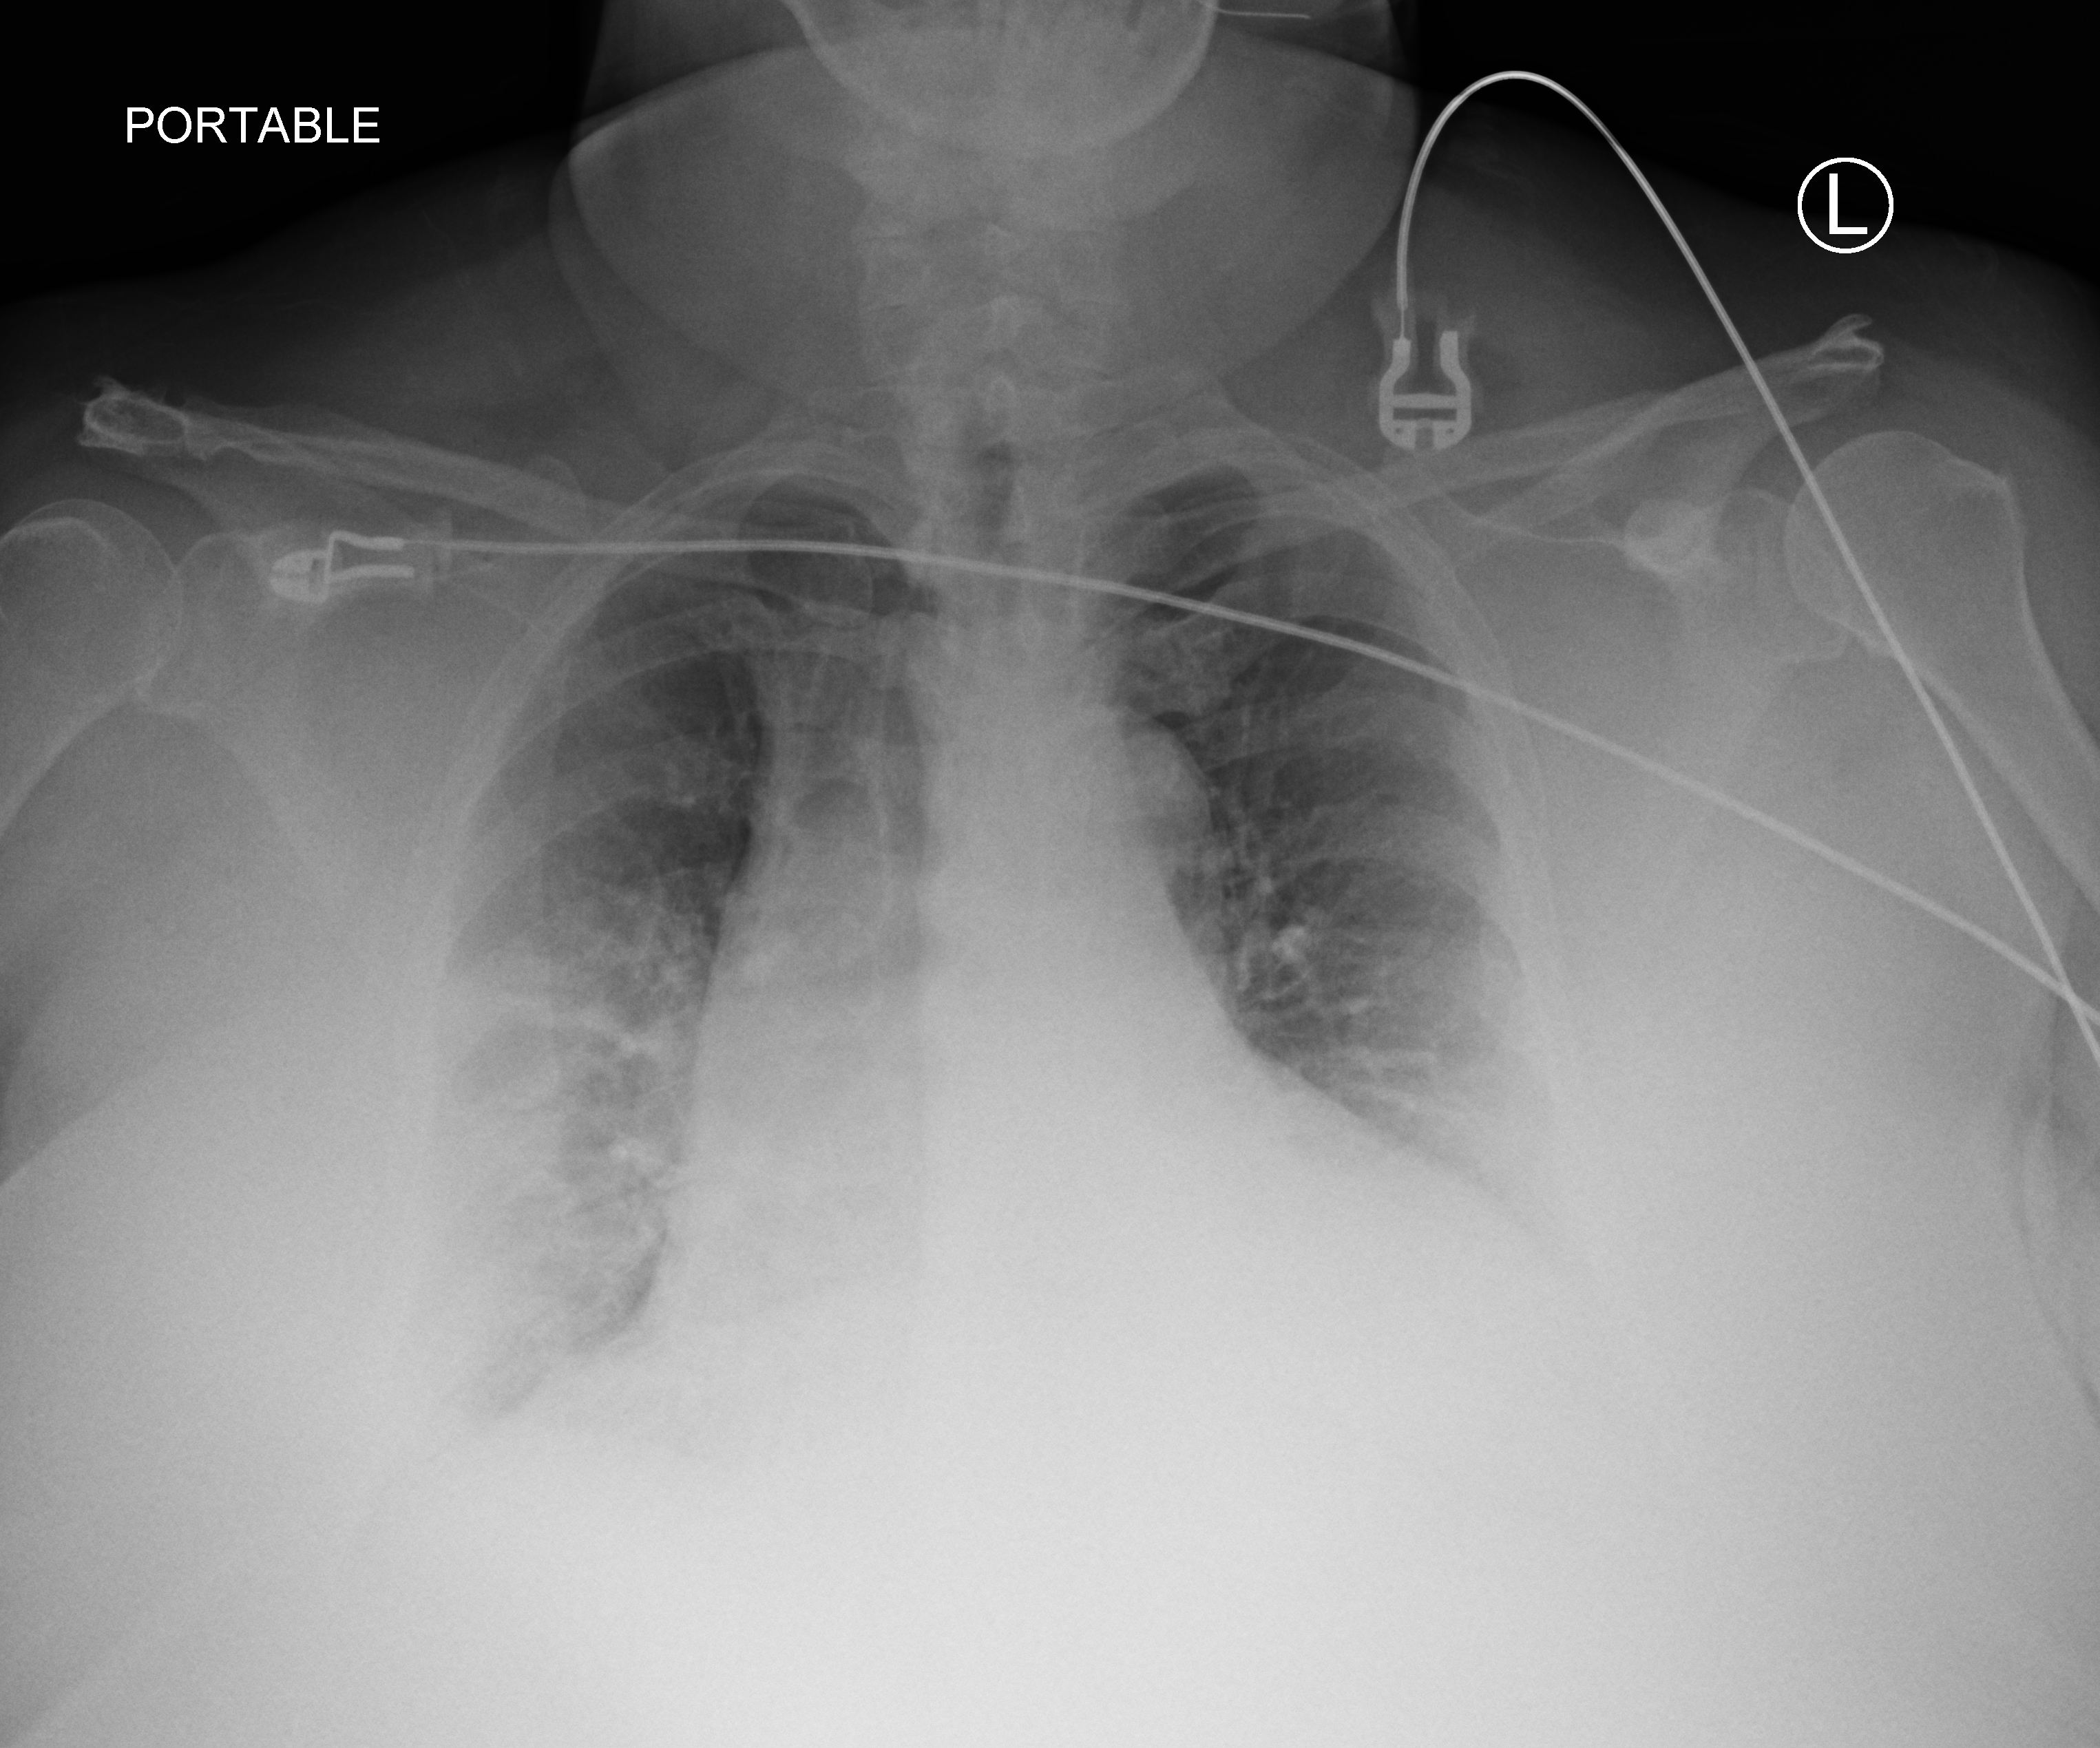
Bedside chest radiograph (computed radiography); anteroposterior (AP) projection. Female patient hospitalised with COVID-19, age 60–74 years.
Admission-level facts for this patient (not findings on this image; timing relative to this image not recorded): COPD (admission record): no; mechanically ventilated during this hospital stay: no.